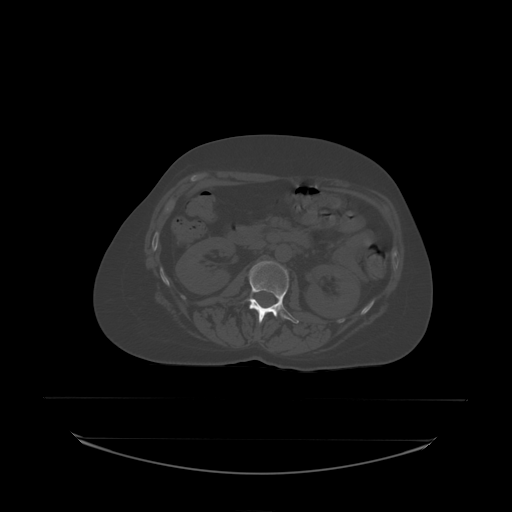
CT including the spine, one axial slice. Position 72 of 242 along the scan axis. Bone window (W 1800 / L 400 HU). 2.5 mm slice thickness. 512 × 512 image matrix. Female patient, age 53 years. From the clinical record (not read from this slice): primary cancer: lung.
Outlined on this slice (semi-automatically segmented with operator editing):
- L2 vertebra: bounding box [x1, y1, x2, y2] px = [248, 261, 299, 324]